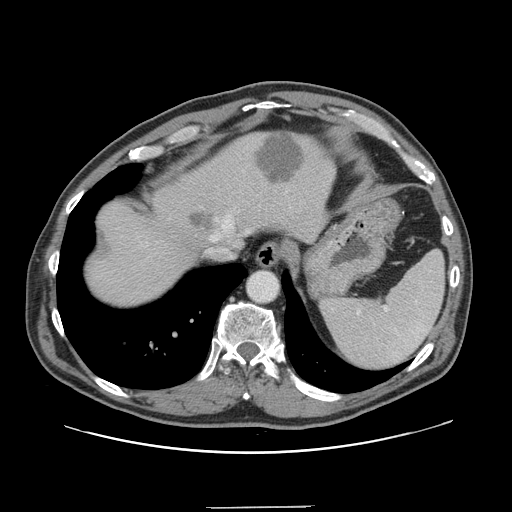
Contrast-enhanced abdominal CT, one axial slice. Slice 123 of 139 in the series (ordered by position). 120 kVp. Intravenous contrast given. Soft-tissue window (W 400 / L 40 HU). 2.5 mm slice thickness. 512 × 512 image matrix, field of view 397 × 397 mm. Male patient, age 64 years. Case-level facts recorded for this patient, not image findings: diagnosis: colorectal cancer liver metastases, imaged before liver resection; multiple liver metastases: yes; largest metastasis: 3.5 cm; chemotherapy before resection: yes.
Annotated regions visible in this slice (manually delineated by an expert):
- hepatic veins: bounding box <223,219,229,228> (left, top, right, bottom; pixels)
- liver: <85,131,333,308>
- planned liver remnant (the part of the liver to remain after resection): <85,138,259,308>
- liver metastasis: <191,213,213,229>
- liver metastasis: <257,134,304,184>